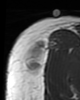
MRI of an extremity soft-tissue mass, one axial slice. Position 32 of 46 along the scan axis. MR volume resampled by the dataset authors to the PET/CT grid (not the native acquisition matrix). 3.27 mm slice thickness. 80 × 100 image matrix, field of view 78 × 98 mm. Female patient. Case-level facts recorded for this patient, not image findings: histological type: synovial sarcoma; grade: intermediate; site of the primary tumour: right thigh.
Structures marked on this image (expert contour drawn on MRI and transferred to this co-registered scan by the dataset authors):
- gross tumour volume including surrounding oedema: bounding box [x1, y1, x2, y2] px = [25, 40, 51, 75]
- gross tumour volume (mass): [23, 42, 45, 75]